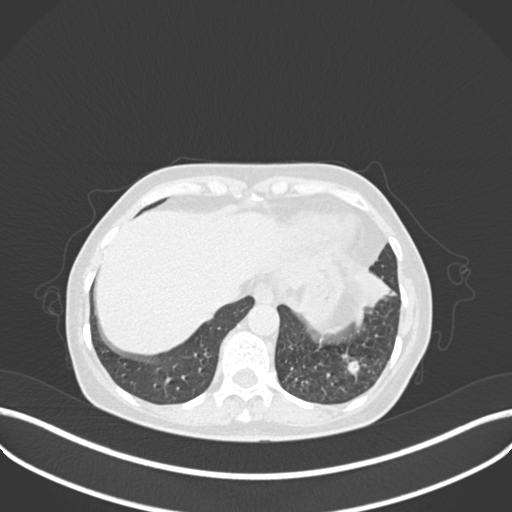
Chest CT, one axial slice. Position 47 of 270 along the scan axis. 120 kVp. Lung window (W 1500 / L -600 HU). 1 mm slice thickness. 512 × 512 image matrix, field of view 400 × 400 mm. Female patient, age 63 years. From the clinical record (not read from this slice): clinical TNM (as recorded): T1b N0 M0.
Annotated regions visible in this slice (rectangle marked by the reading radiologist):
- lung tumour (recorded histology: adenocarcinoma): bounding box [x1, y1, x2, y2] px = [344, 254, 391, 309]